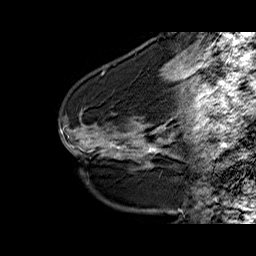
Breast MRI (dynamic contrast-enhanced), one sagittal slice. Position 18 of 60 along the scan axis. Dynamic contrast-enhanced series, time point 2 of 6 at this slice position (early post-contrast). 1.5 T. TE 6.3 ms, TR 32.5 ms. 4 mm slice thickness. 256 × 256 image matrix, field of view 200 × 200 mm. Female patient. Case-level facts recorded for this patient, not image findings: setting: breast cancer imaged before/during neoadjuvant chemotherapy; receptor status: HR-positive, HER2-negative.
Structures marked on this image (semi-automatically segmented with operator editing):
- analysis volume of interest (the breast-tissue region the enhancement analysis was run in; not a lesion): bounding box <94,113,161,164> (left, top, right, bottom; pixels)
- tumour enhancement mask (voxels above the 100 % enhancement threshold inside the analysis volume of interest): <147,147,156,153>